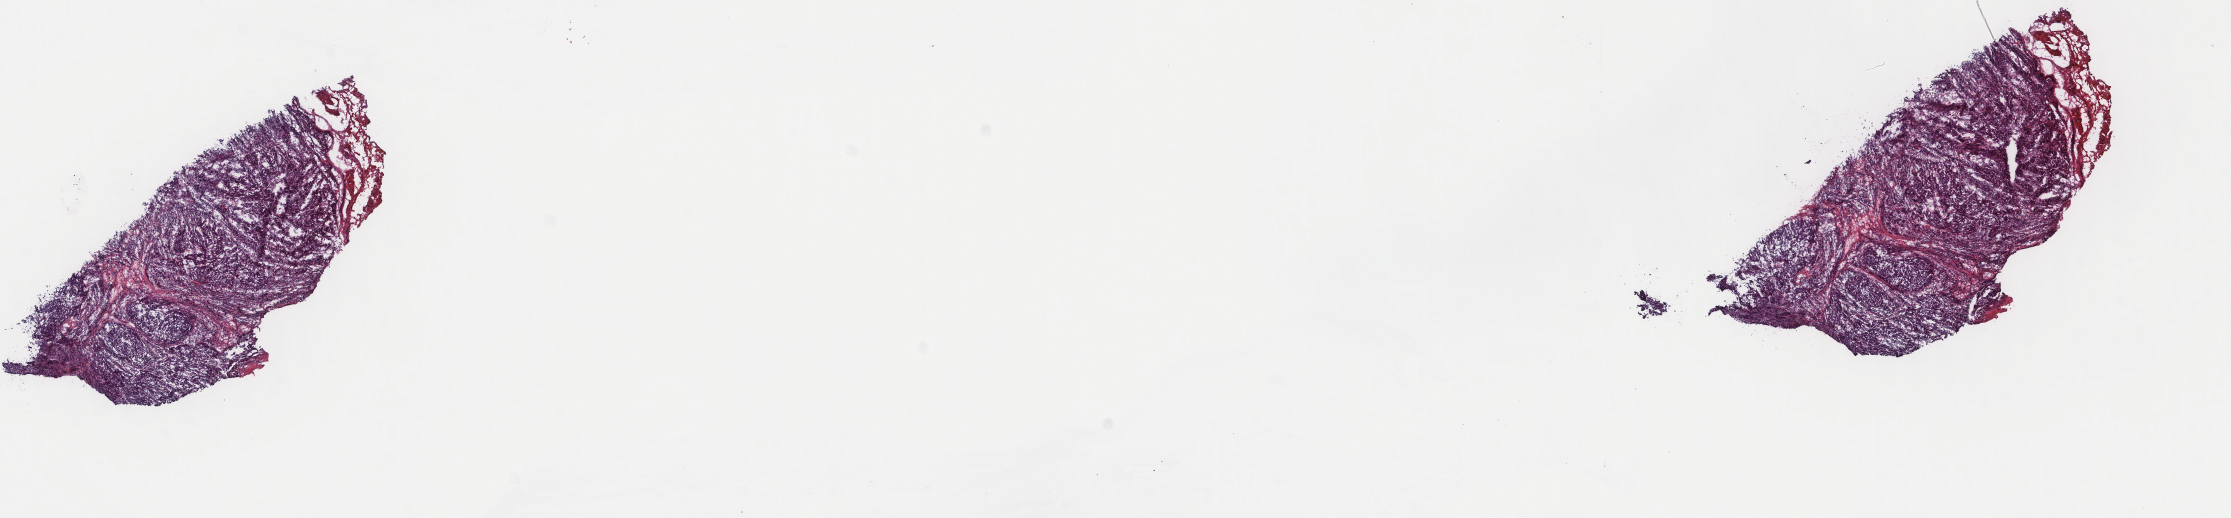
Whole-slide histology image, H&E, whole scanned area (about 17.7 x 4.1 mm, from a 40x scan) shown as a low-resolution overview; frozen section from the top of the tissue portion; head and neck, primary tumour sample. Male, age 54 years at initial diagnosis. Histologic grade: G3 (poorly differentiated). Slide review estimates, as recorded: tumour cells 70%, tumour nuclei 60%, normal cells 0%, stromal cells 30%, necrosis 0%. Inflammatory infiltration, as recorded: lymphocyte infiltration 30%, monocyte infiltration 0%, neutrophil infiltration 0%.
* AJCC pathologic stage: IVA (6th edition)
* diagnosis: Basaloid squamous cell carcinoma (tonsil, NOS)